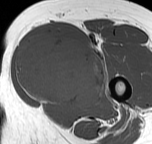
MRI of an extremity soft-tissue mass, one axial slice; slice 31 of 57 in the series (ordered by position); MR volume resampled by the dataset authors to the PET/CT grid (not the native acquisition matrix); 3.27 mm slice thickness; 152 × 144 image matrix, field of view 148 × 141 mm. Female patient. Case-level facts recorded for this patient, not image findings: histological type: pleiomorphic leiomyosarcoma; grade: intermediate; site of the primary tumour: left thigh.
Structures marked on this image (expert contour drawn on MRI and transferred to this co-registered scan by the dataset authors):
- gross tumour volume including surrounding oedema: bounding box <15,35,105,107> (left, top, right, bottom; pixels)
- gross tumour volume (mass): <15,37,105,107>